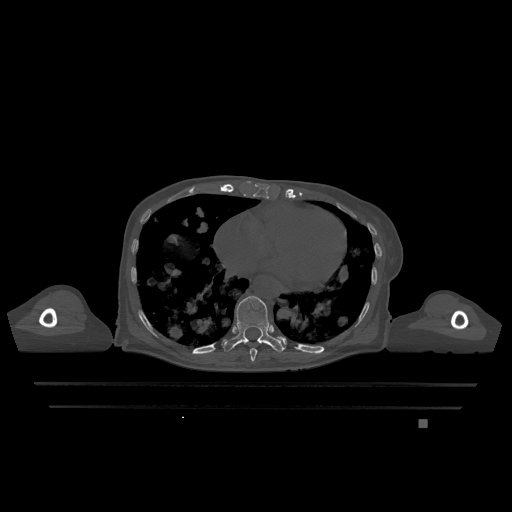
CT including the spine, one axial slice; position 657 of 1317 along the scan axis; bone window (W 1800 / L 400 HU); 0.5 mm slice thickness; 512 × 512 image matrix. Female patient, age 74 years. Case-level facts recorded for this patient, not image findings: primary cancer: lung; vertebrae with lytic lesions (as recorded): T1, T4, T5, T6, L4, L5.
Structures marked on this image (semi-automatic segmentation, software-assisted and operator-edited):
- T10 vertebra: bounding box (x1, y1, x2, y2) in pixels: (223, 296, 284, 353)
- T9 vertebra: (249, 348, 257, 362)